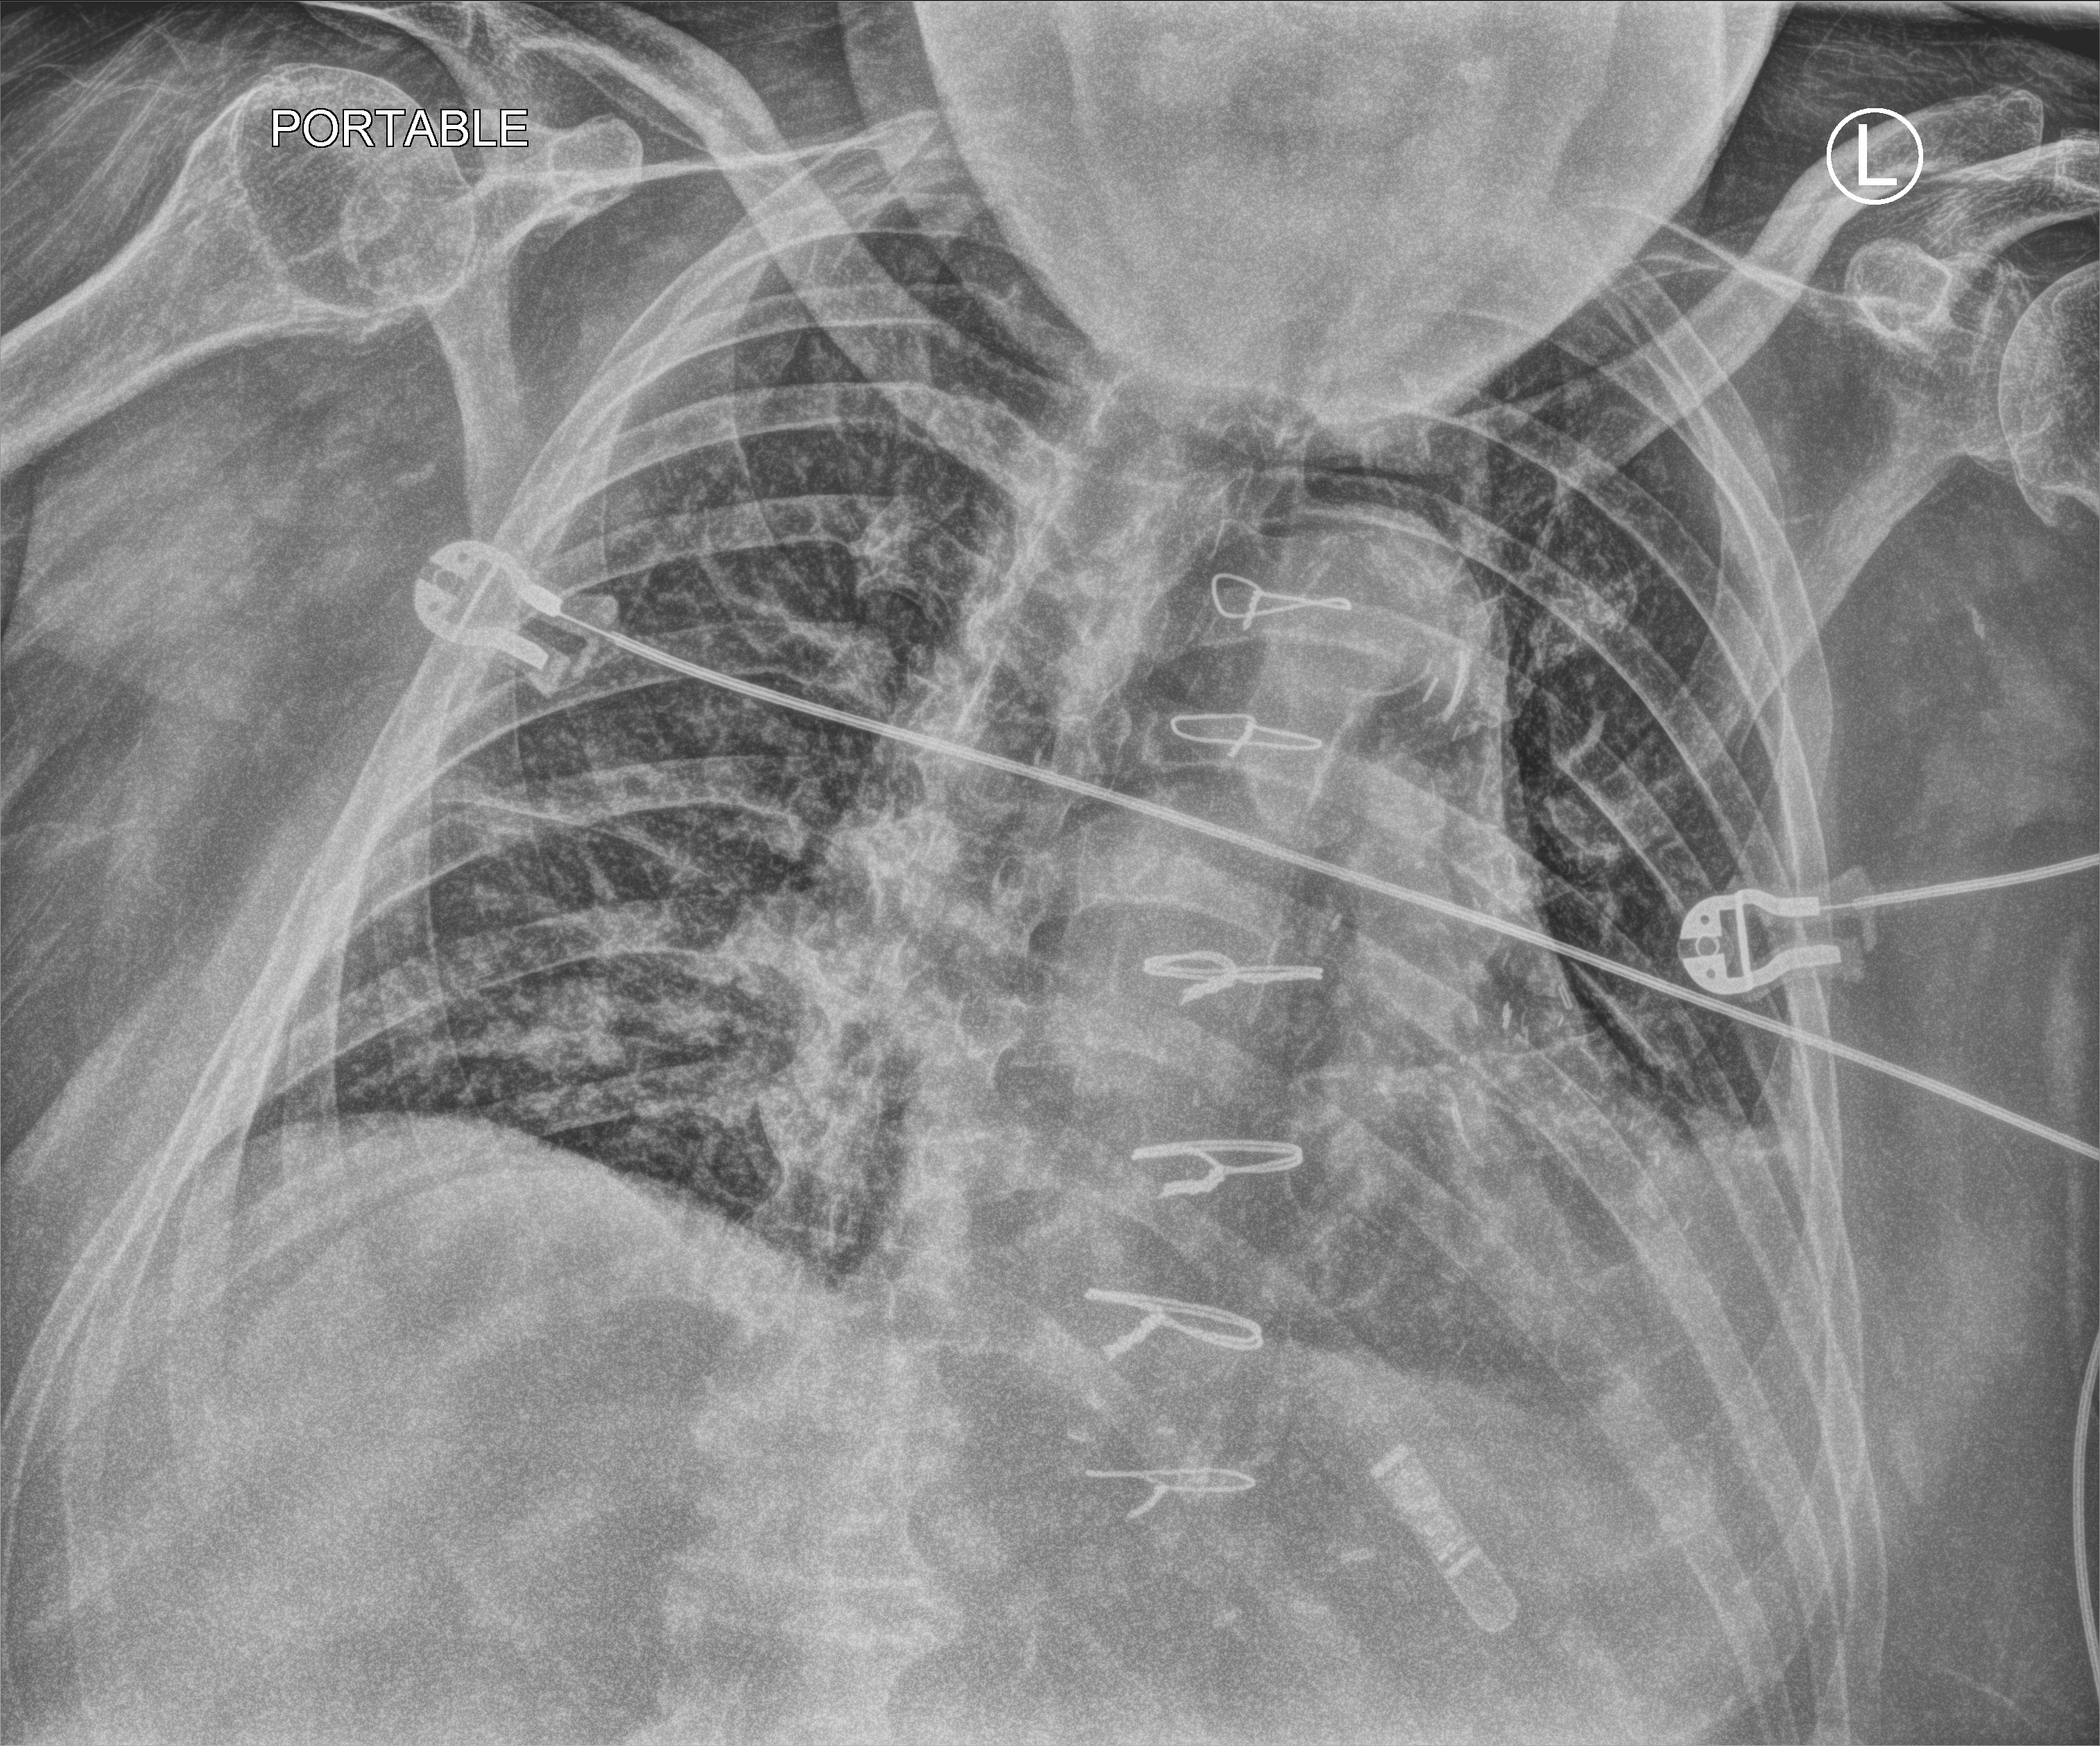
Portable chest radiograph; anteroposterior (AP) projection. Male patient hospitalised with COVID-19, age 60–74 years.
Admission-level facts for this patient (not findings on this image; timing relative to this image not recorded):
- mechanically ventilated during this hospital stay: no